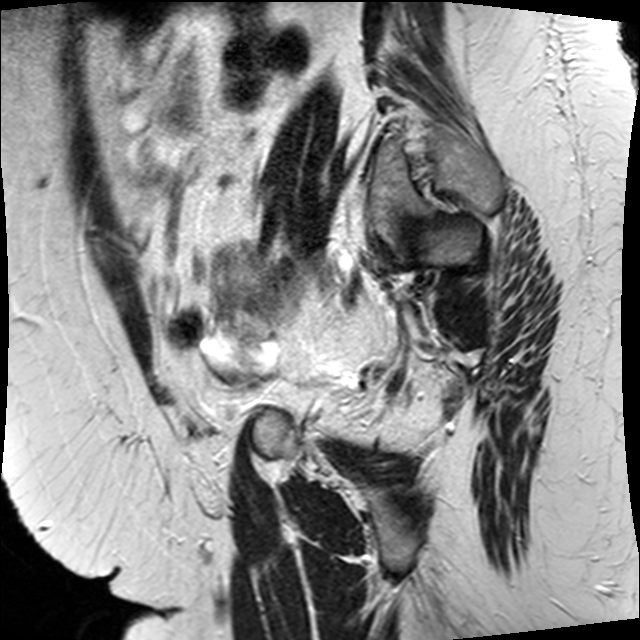
Pelvic MRI for cervical cancer, one sagittal slice; slice 28 of 34 in the series (ordered by position); T2-weighted; 1.5 T; TE 89 ms, TR 3320 ms; 4 mm slice thickness; 640 × 640 image matrix, field of view 260 × 260 mm. Female patient, age 50 years.
Annotated regions visible in this slice (expert manual segmentation):
- uterus and cervix: box from (x=212, y=244) to (x=280, y=316) px